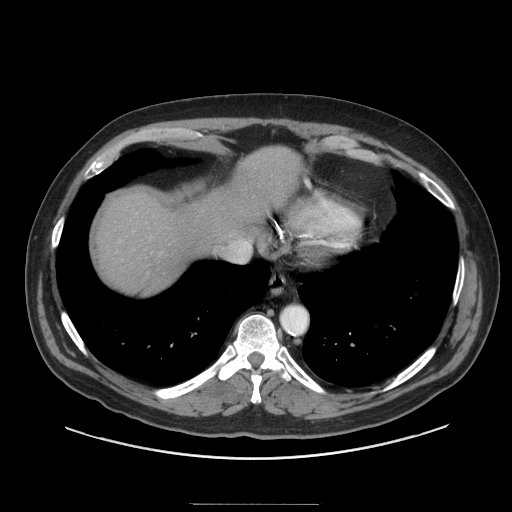
Contrast-enhanced abdominal CT (liver protocol), one axial slice. Position 82 of 91 along the scan axis. Reconstruction kernel STANDARD. 140 kVp. Soft-tissue window (W 400 / L 40 HU). 2.5 mm slice thickness. 512 × 512 image matrix, field of view 440 × 440 mm. Case-level facts recorded for this patient, not image findings: diagnosis: hepatocellular carcinoma (patient treated with transarterial chemoembolisation; whether this scan precedes or follows treatment is not stated here); TNM stage (as recorded): Stage-I; Child-Pugh class: A; tumour differentiation: well differentiated; tumour nodularity: uninodular.
Structures marked on this image (semi-automatically segmented with operator editing):
- liver parenchyma outside the tumour (the mass and vessels are separate outlines, so this box may not span the whole liver): bounding box [x1, y1, x2, y2] px = [96, 146, 300, 294]